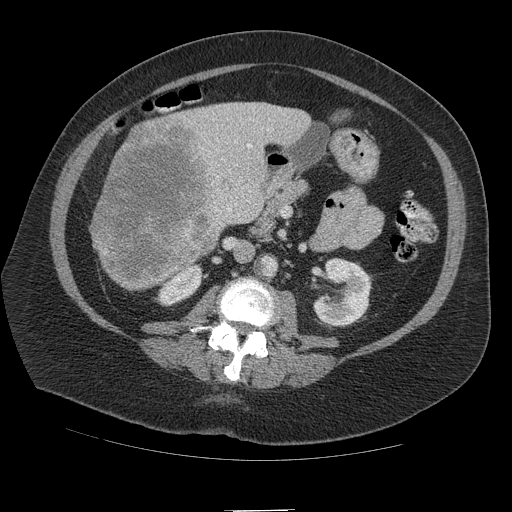
Contrast-enhanced abdominal CT (liver protocol), one axial slice; position 41 of 109 along the scan axis; 140 kVp; soft-tissue window (W 400 / L 40 HU); 512 × 512 image matrix, field of view 420 × 420 mm. Case-level facts recorded for this patient, not image findings: diagnosis: hepatocellular carcinoma (patient treated with transarterial chemoembolisation; whether this scan precedes or follows treatment is not stated here); TNM stage (as recorded): Stage-IVB; Child-Pugh class: A.
Annotated regions visible in this slice (semi-automatically segmented with operator editing):
- liver parenchyma outside the tumour (the mass and vessels are separate outlines, so this box may not span the whole liver): bounding box [x1, y1, x2, y2] px = [96, 102, 310, 236]
- mass: [89, 115, 220, 291]
- liver vessels: [216, 129, 269, 211]